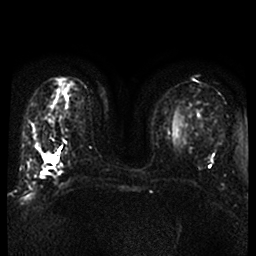
Breast MRI, one axial slice. Position 18 of 52 along the scan axis. Diffusion-weighted series; image 2 of 4 stored at this slice position (different b-values; order by instance number). 1.5 T. 4 mm slice thickness. 256 × 256 image matrix, field of view 320 × 320 mm. Female patient.
Annotated regions visible in this slice (expert manual segmentation):
- tumour on diffusion-weighted imaging: bounding box (x1, y1, x2, y2) in pixels: (44, 153, 54, 162)